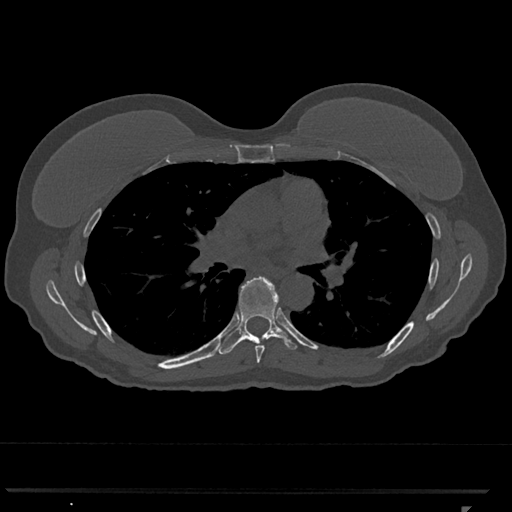
CT including the spine, one axial slice. Position 731 of 793 along the scan axis. Reconstruction kernel Br40s/3. 120 kVp. Bone window (W 1800 / L 400 HU). 0.5 mm slice thickness. 512 × 512 image matrix, field of view 380 × 380 mm. Patient: female, 62 years. Case-level facts recorded for this patient, not image findings: primary cancer: renal.
Outlined on this slice (semi-automatic segmentation, software-assisted and operator-edited):
- T6 vertebra: bounding box (x1, y1, x2, y2) in pixels: (255, 342, 265, 363)
- T7 vertebra: (216, 277, 297, 354)